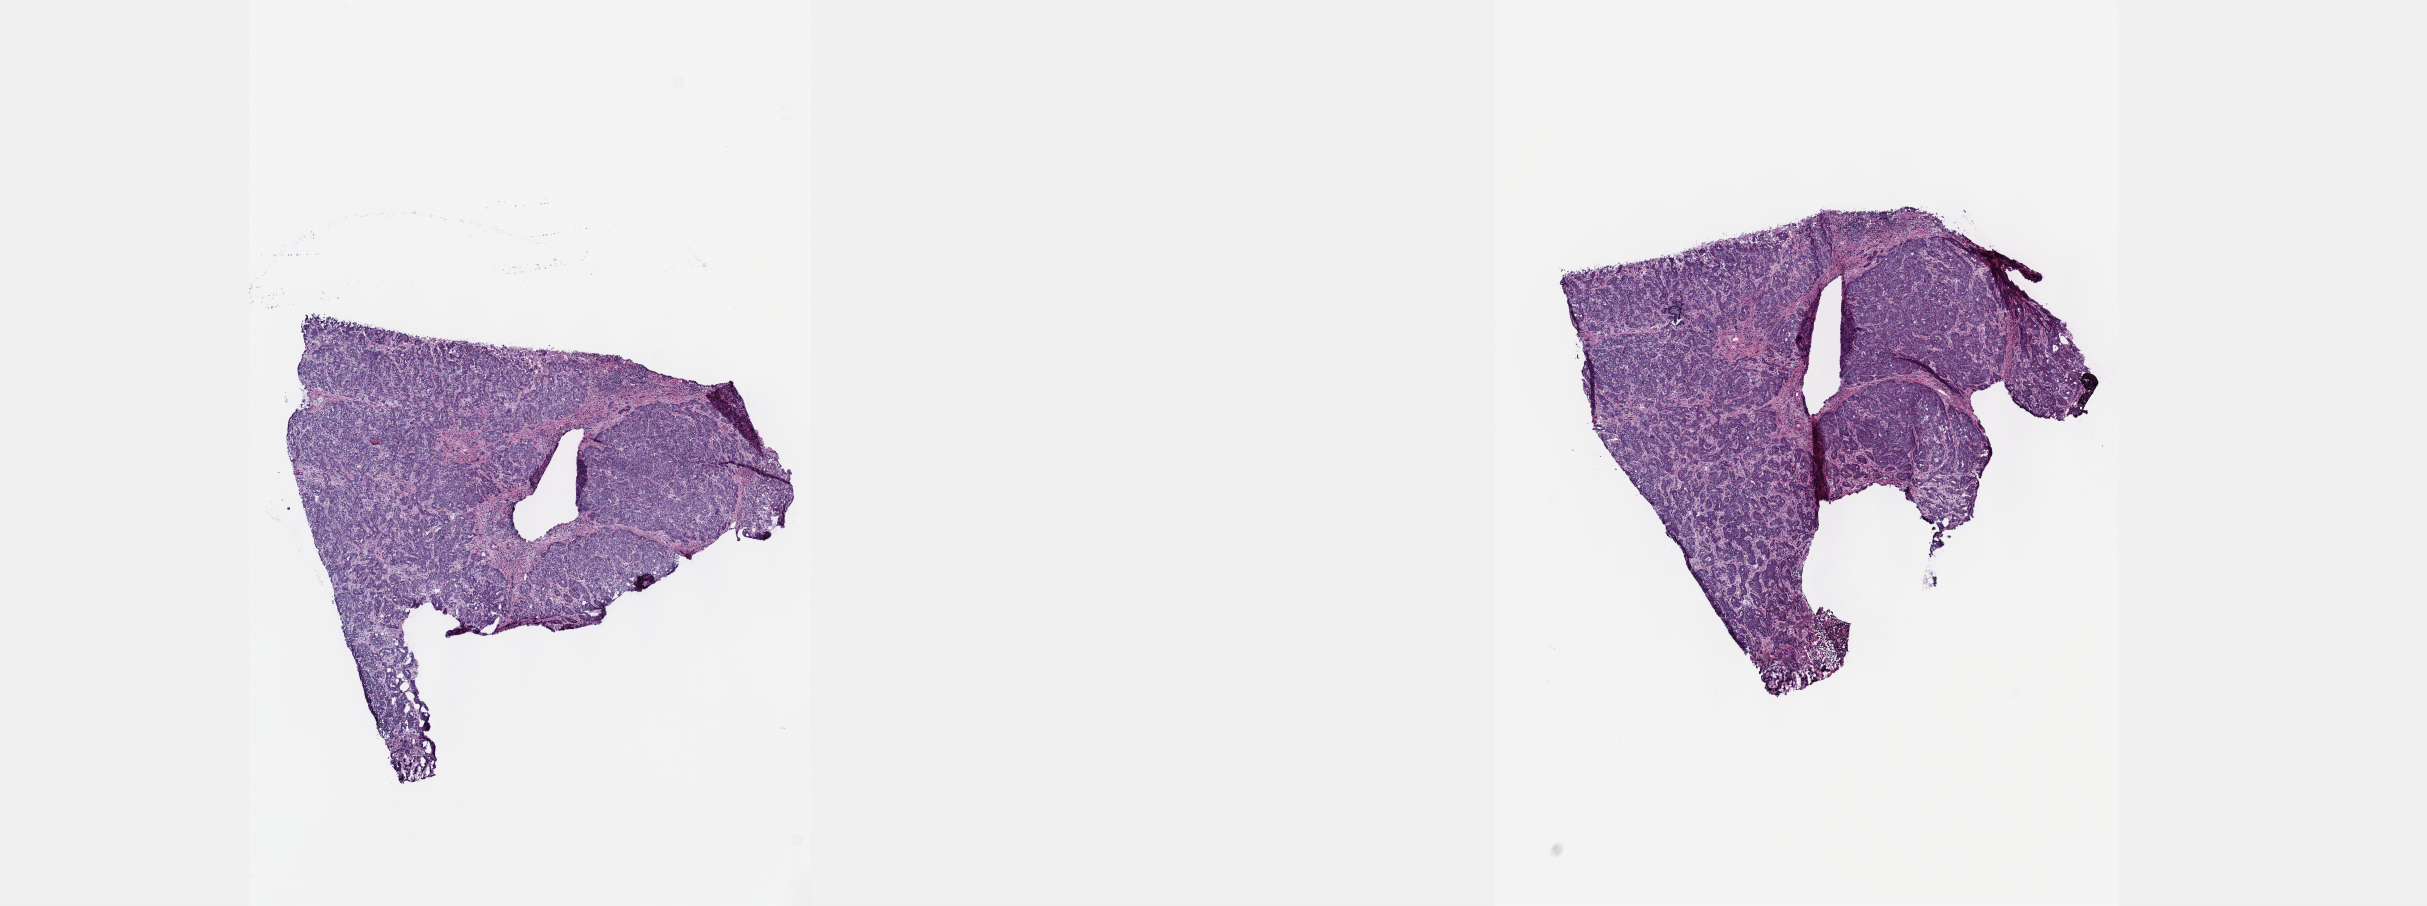
Digitized H&E tissue section (whole slide) — low-resolution overview of the scanned area, about 19.6 x 7.3 mm; frozen section; sample: primary tumour, liver. Male patient; age at initial diagnosis 51 years. Histologic grade: G2 (moderately differentiated). Slide review estimates, as recorded: tumour cells 100%, tumour nuclei 75%, normal cells 0%, stromal cells 0%, necrosis 0%. Infiltration values recorded for this section: lymphocyte infiltration 0%, monocyte infiltration 0%, neutrophil infiltration 0%.
• diagnosis: Hepatocellular carcinoma, NOS